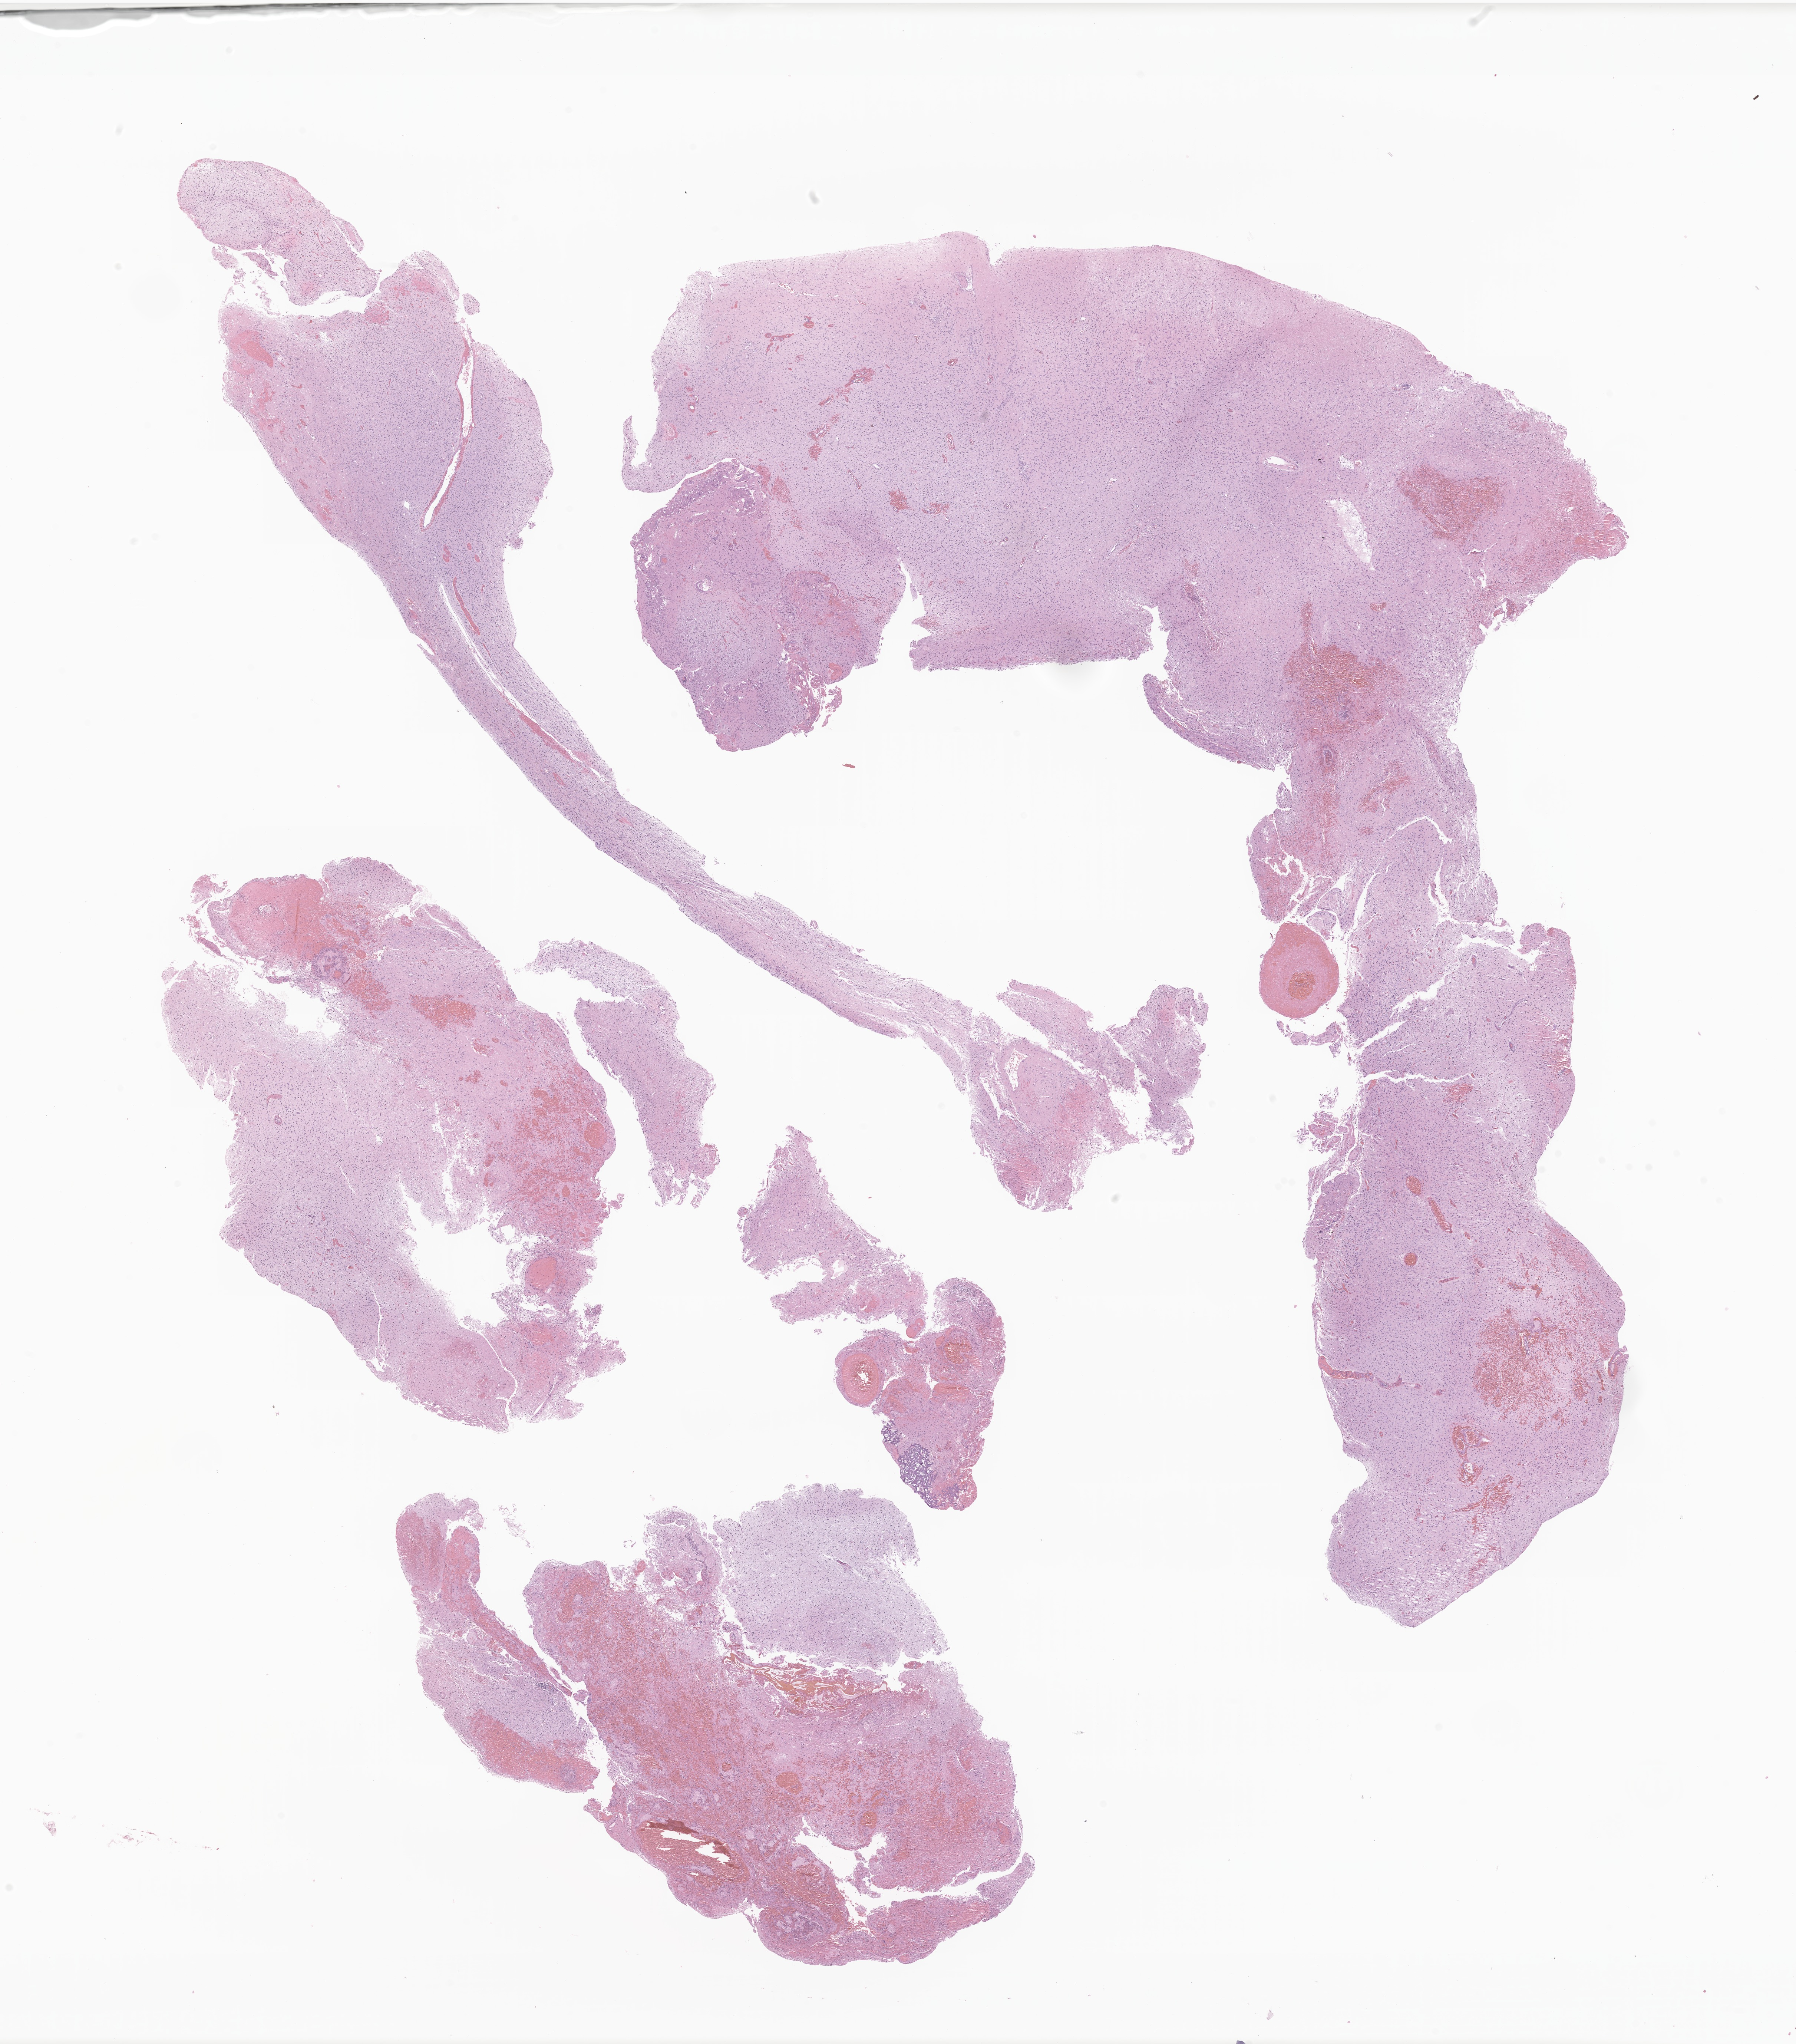
Hematoxylin and eosin (H&E) whole-slide image of tumor tissue from the cerebellum — shown as a low-resolution overview of the whole scanned area (about 20.4 x 23.2 mm), FFPE section. Patient: male, age 193 months (16 years 1 month).
* diagnosis (ICD-O-3 morphology term): Neoplasm, benign